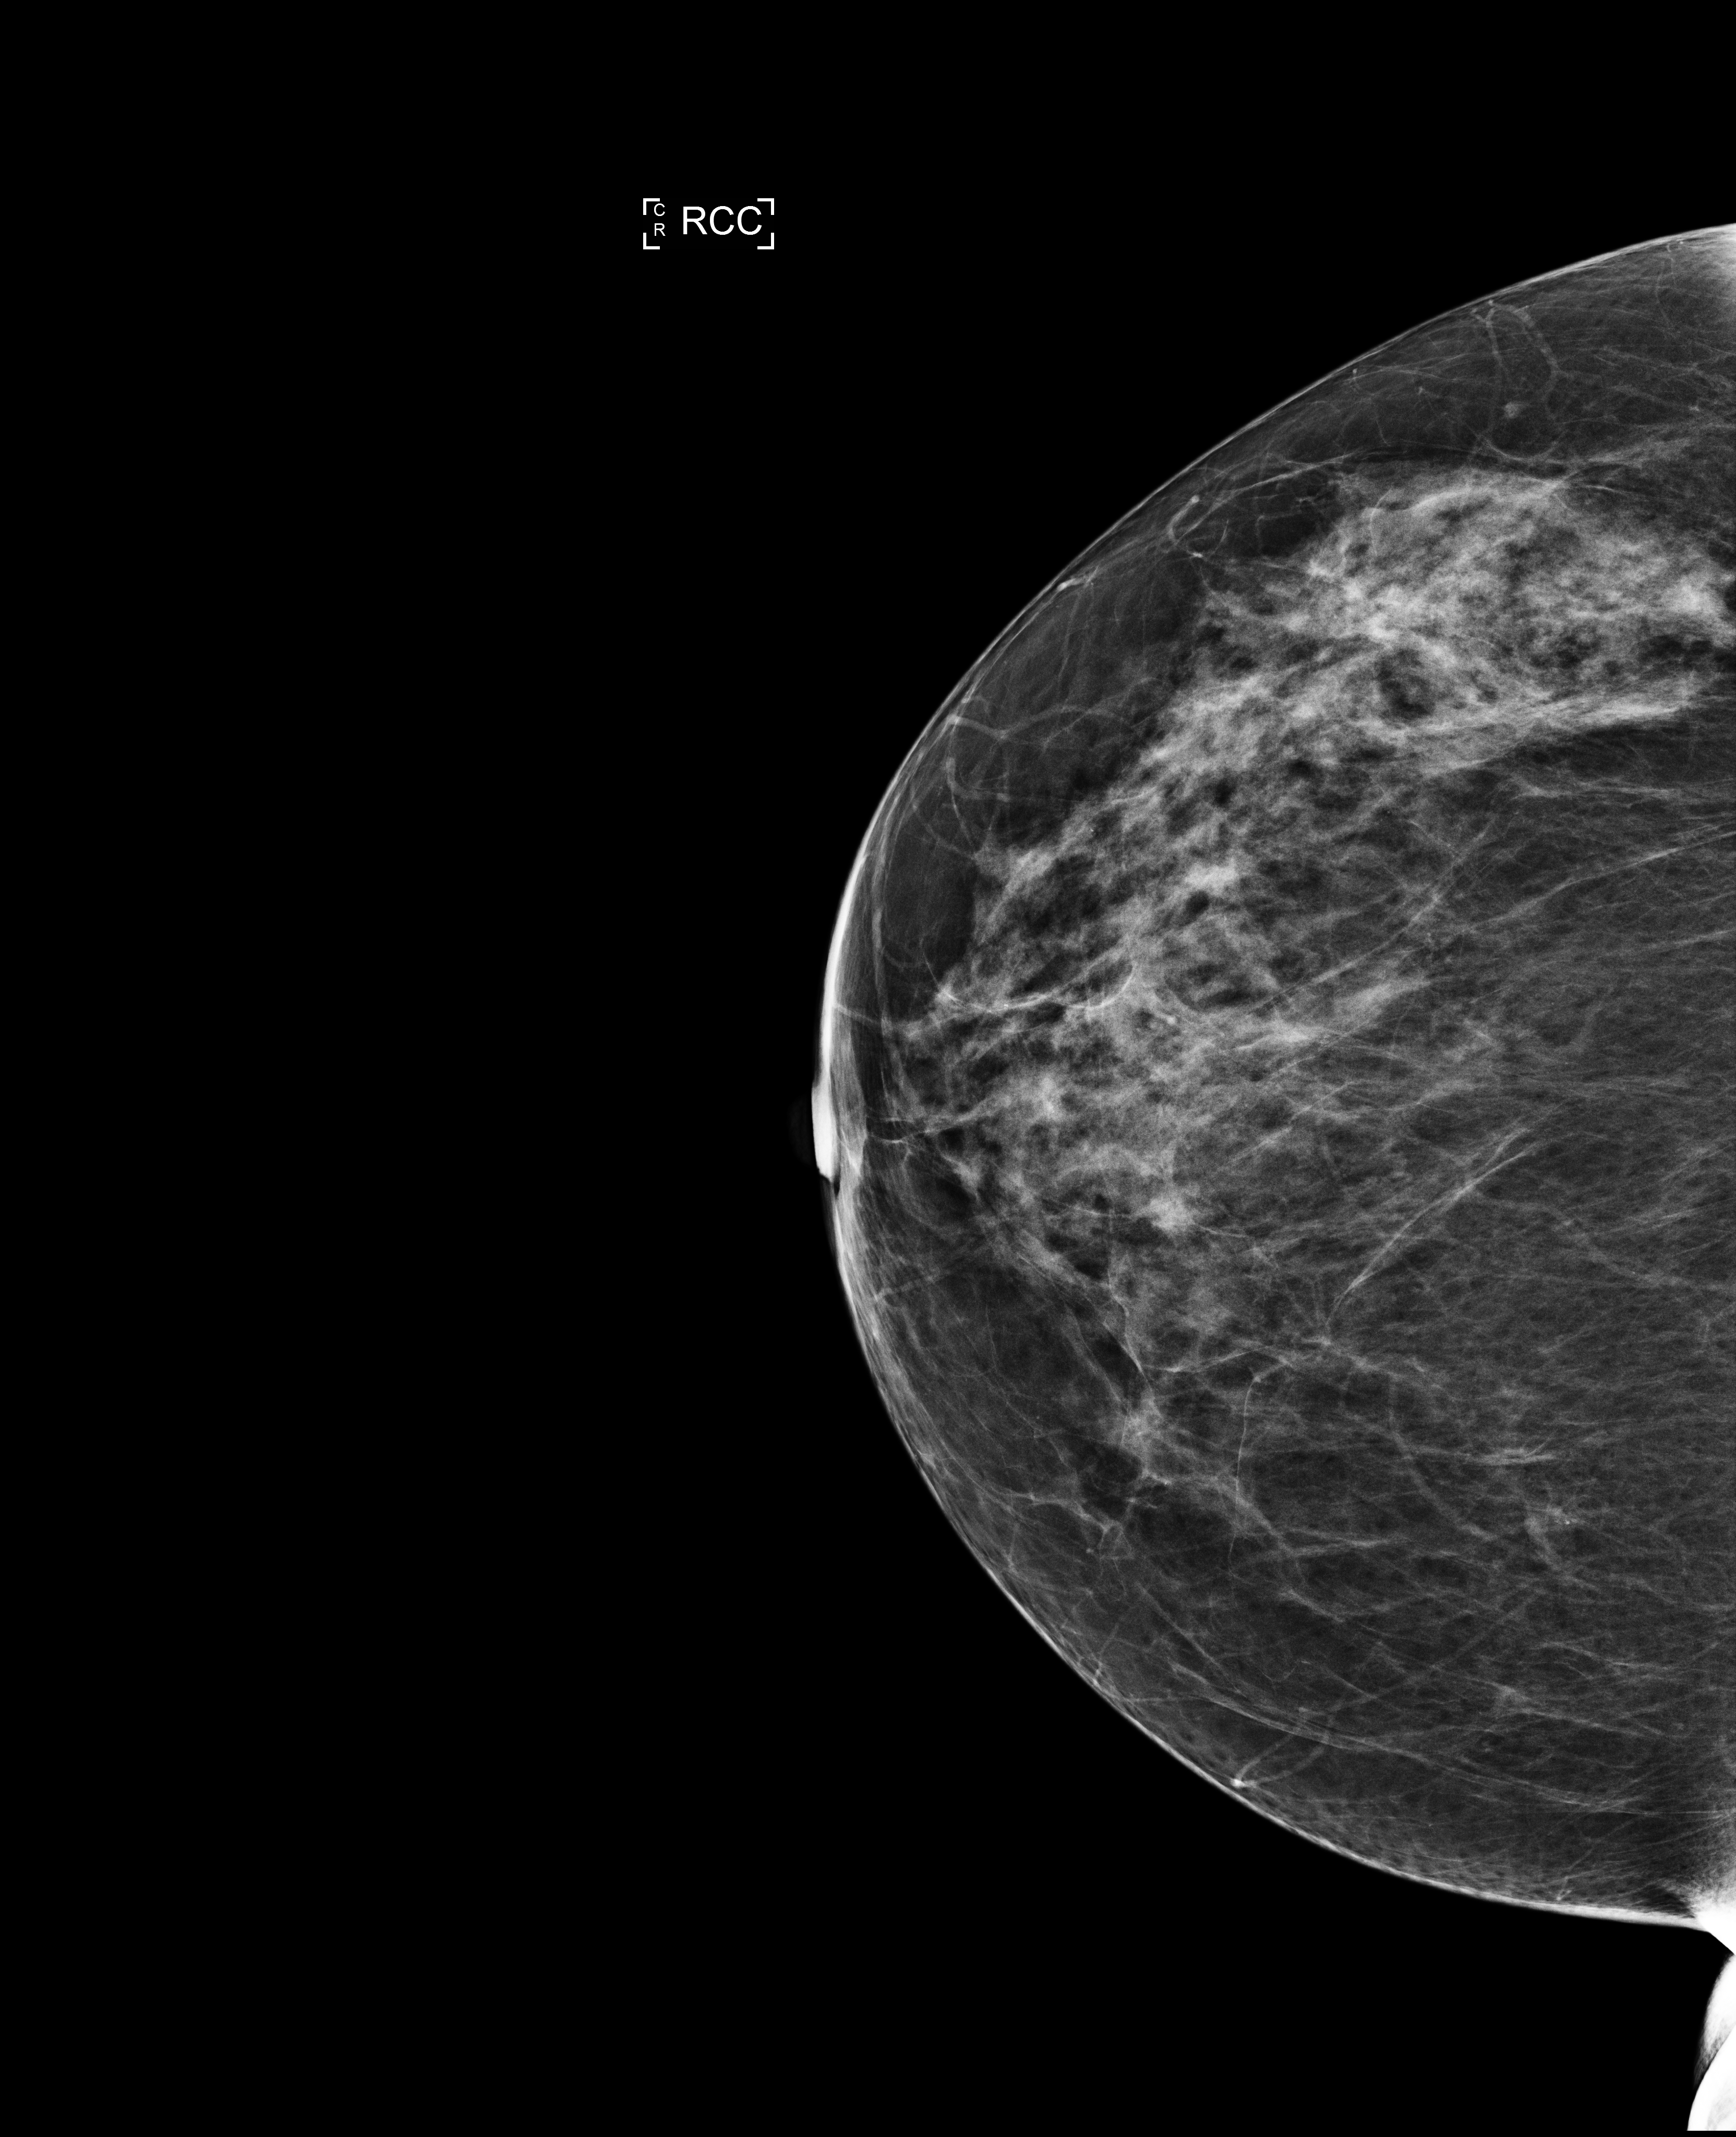
Annual screening mammography examination, compressed breast thickness 52 mm. Female patient, age 58 years.
Image type: full-field digital mammogram. Breast: right. Projection: craniocaudal (CC) view.